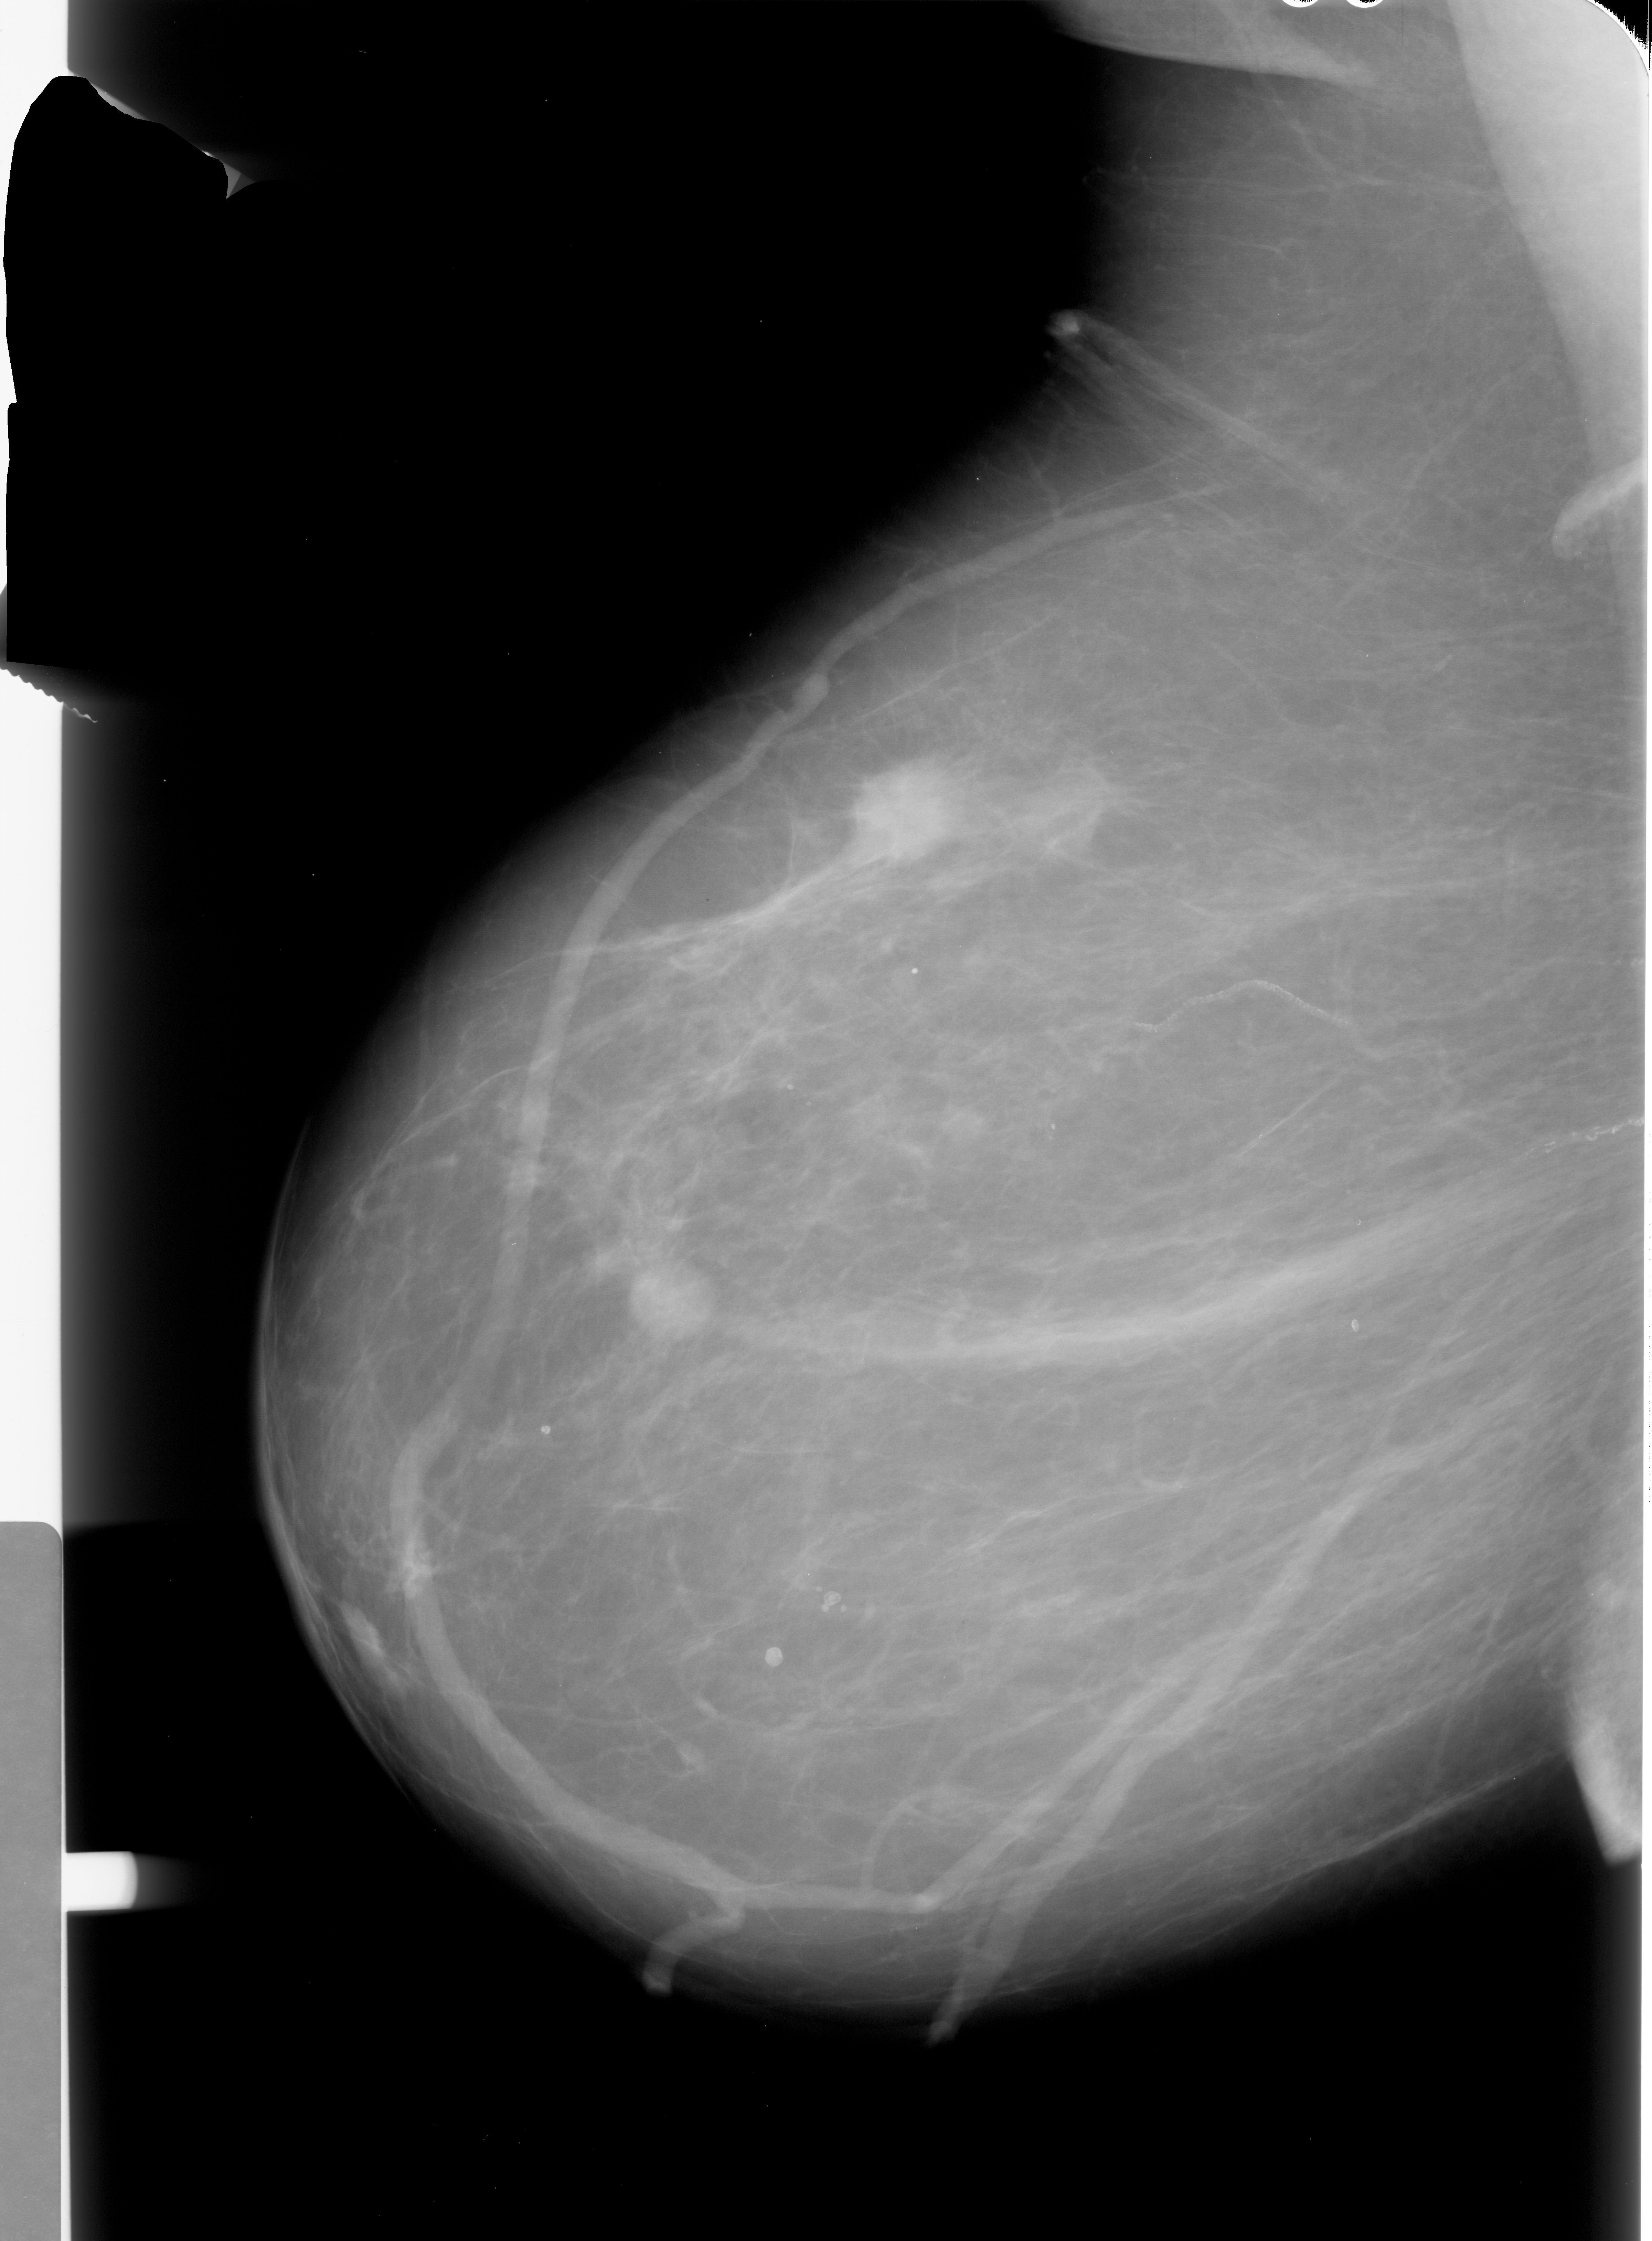
Scanned film-screen mammogram. Left breast. MLO view. 1652 × 2241 image matrix.
Expert-marked regions of interest on this image (one box per marked abnormality):
- mass, shape irregular, margins spiculated; BI-RADS assessment category 5; pathology (as recorded): malignant: bounding box (x1, y1, x2, y2) in pixels: (848, 757, 969, 866)